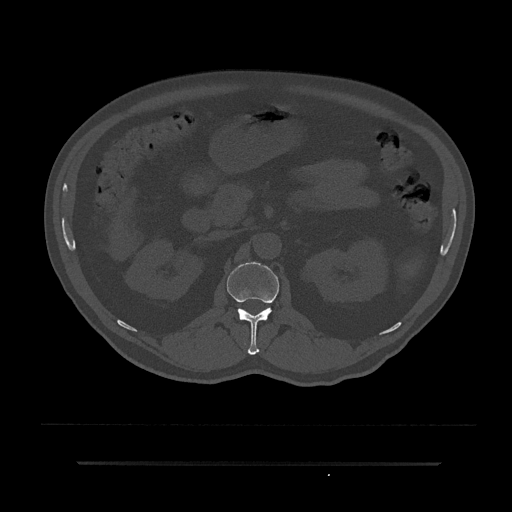
CT including the spine, one axial slice; slice 136 of 797 in the series (ordered by position); 120 kVp; bone window (W 1800 / L 400 HU); 0.5 mm slice thickness; 512 × 512 image matrix, field of view 464 × 464 mm. Patient: male, 59 years. Case-level facts recorded for this patient, not image findings: primary cancer: bile ducts.
Outlined on this slice (semi-automatically segmented with operator editing):
- L1 vertebra: bounding box <227,262,279,355> (left, top, right, bottom; pixels)